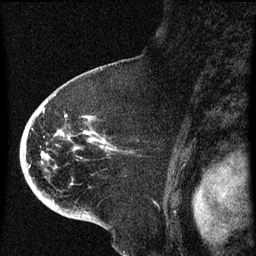
Breast MRI (dynamic contrast-enhanced), one sagittal slice. Position 45 of 60 along the scan axis. Dynamic contrast-enhanced series, image 2 of 4 at this slice position (ordered by acquisition). 1.5 T. TE 4.2 ms, TR 8 ms. 2 mm slice thickness. 256 × 256 image matrix. Patient: female, 71 years.
Annotated regions visible in this slice (semi-automatic segmentation, software-assisted and operator-edited):
- analysis volume of interest (the breast-tissue region the enhancement analysis was run in; not a lesion): bounding box [x1, y1, x2, y2] px = [32, 86, 132, 205]
- tumour enhancement mask (voxels above the 70 % enhancement threshold inside the analysis volume of interest): [43, 110, 116, 151]